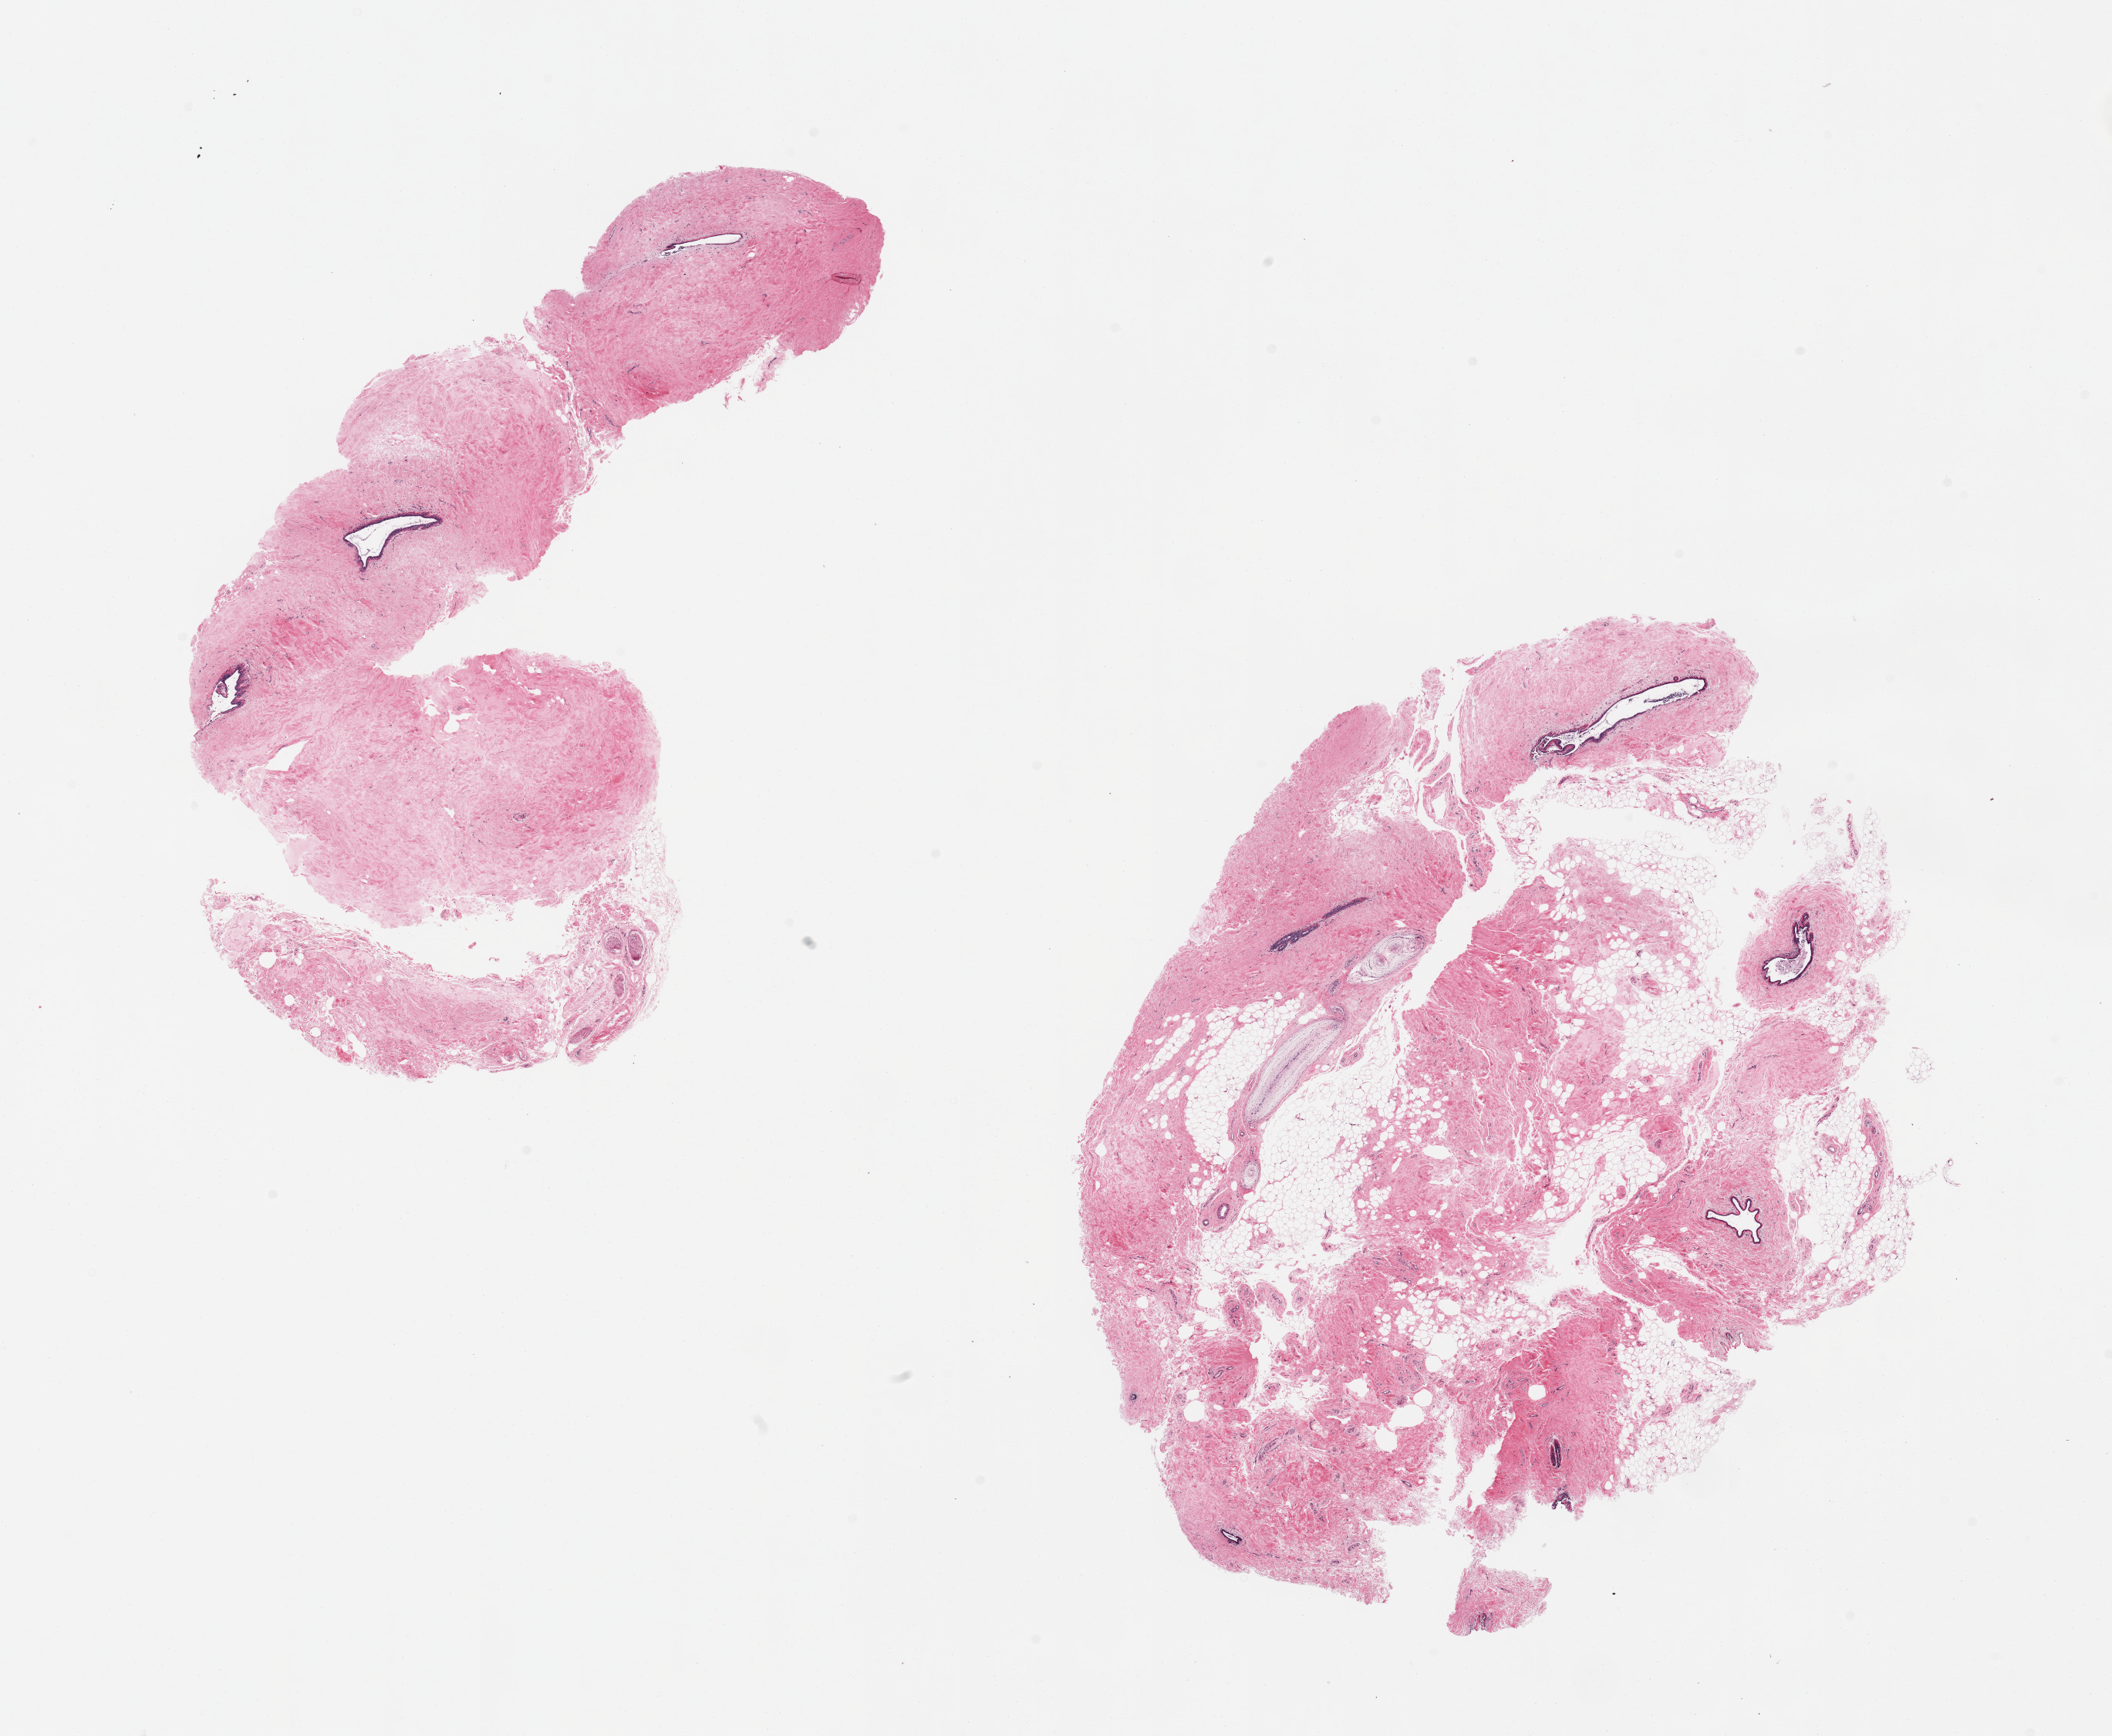
Whole-slide image, haematoxylin and eosin stain — shown as a low-resolution overview of the whole scanned area (about 21.7 x 17.8 mm, slide scanned at 20x). PAXgene-fixed, paraffin-embedded tissue. Target tissue: breast. Tissue donor sample. Female donor.
Reviewer comment on this tissue sample: 2 pieces; atrophic ducts no lobules.